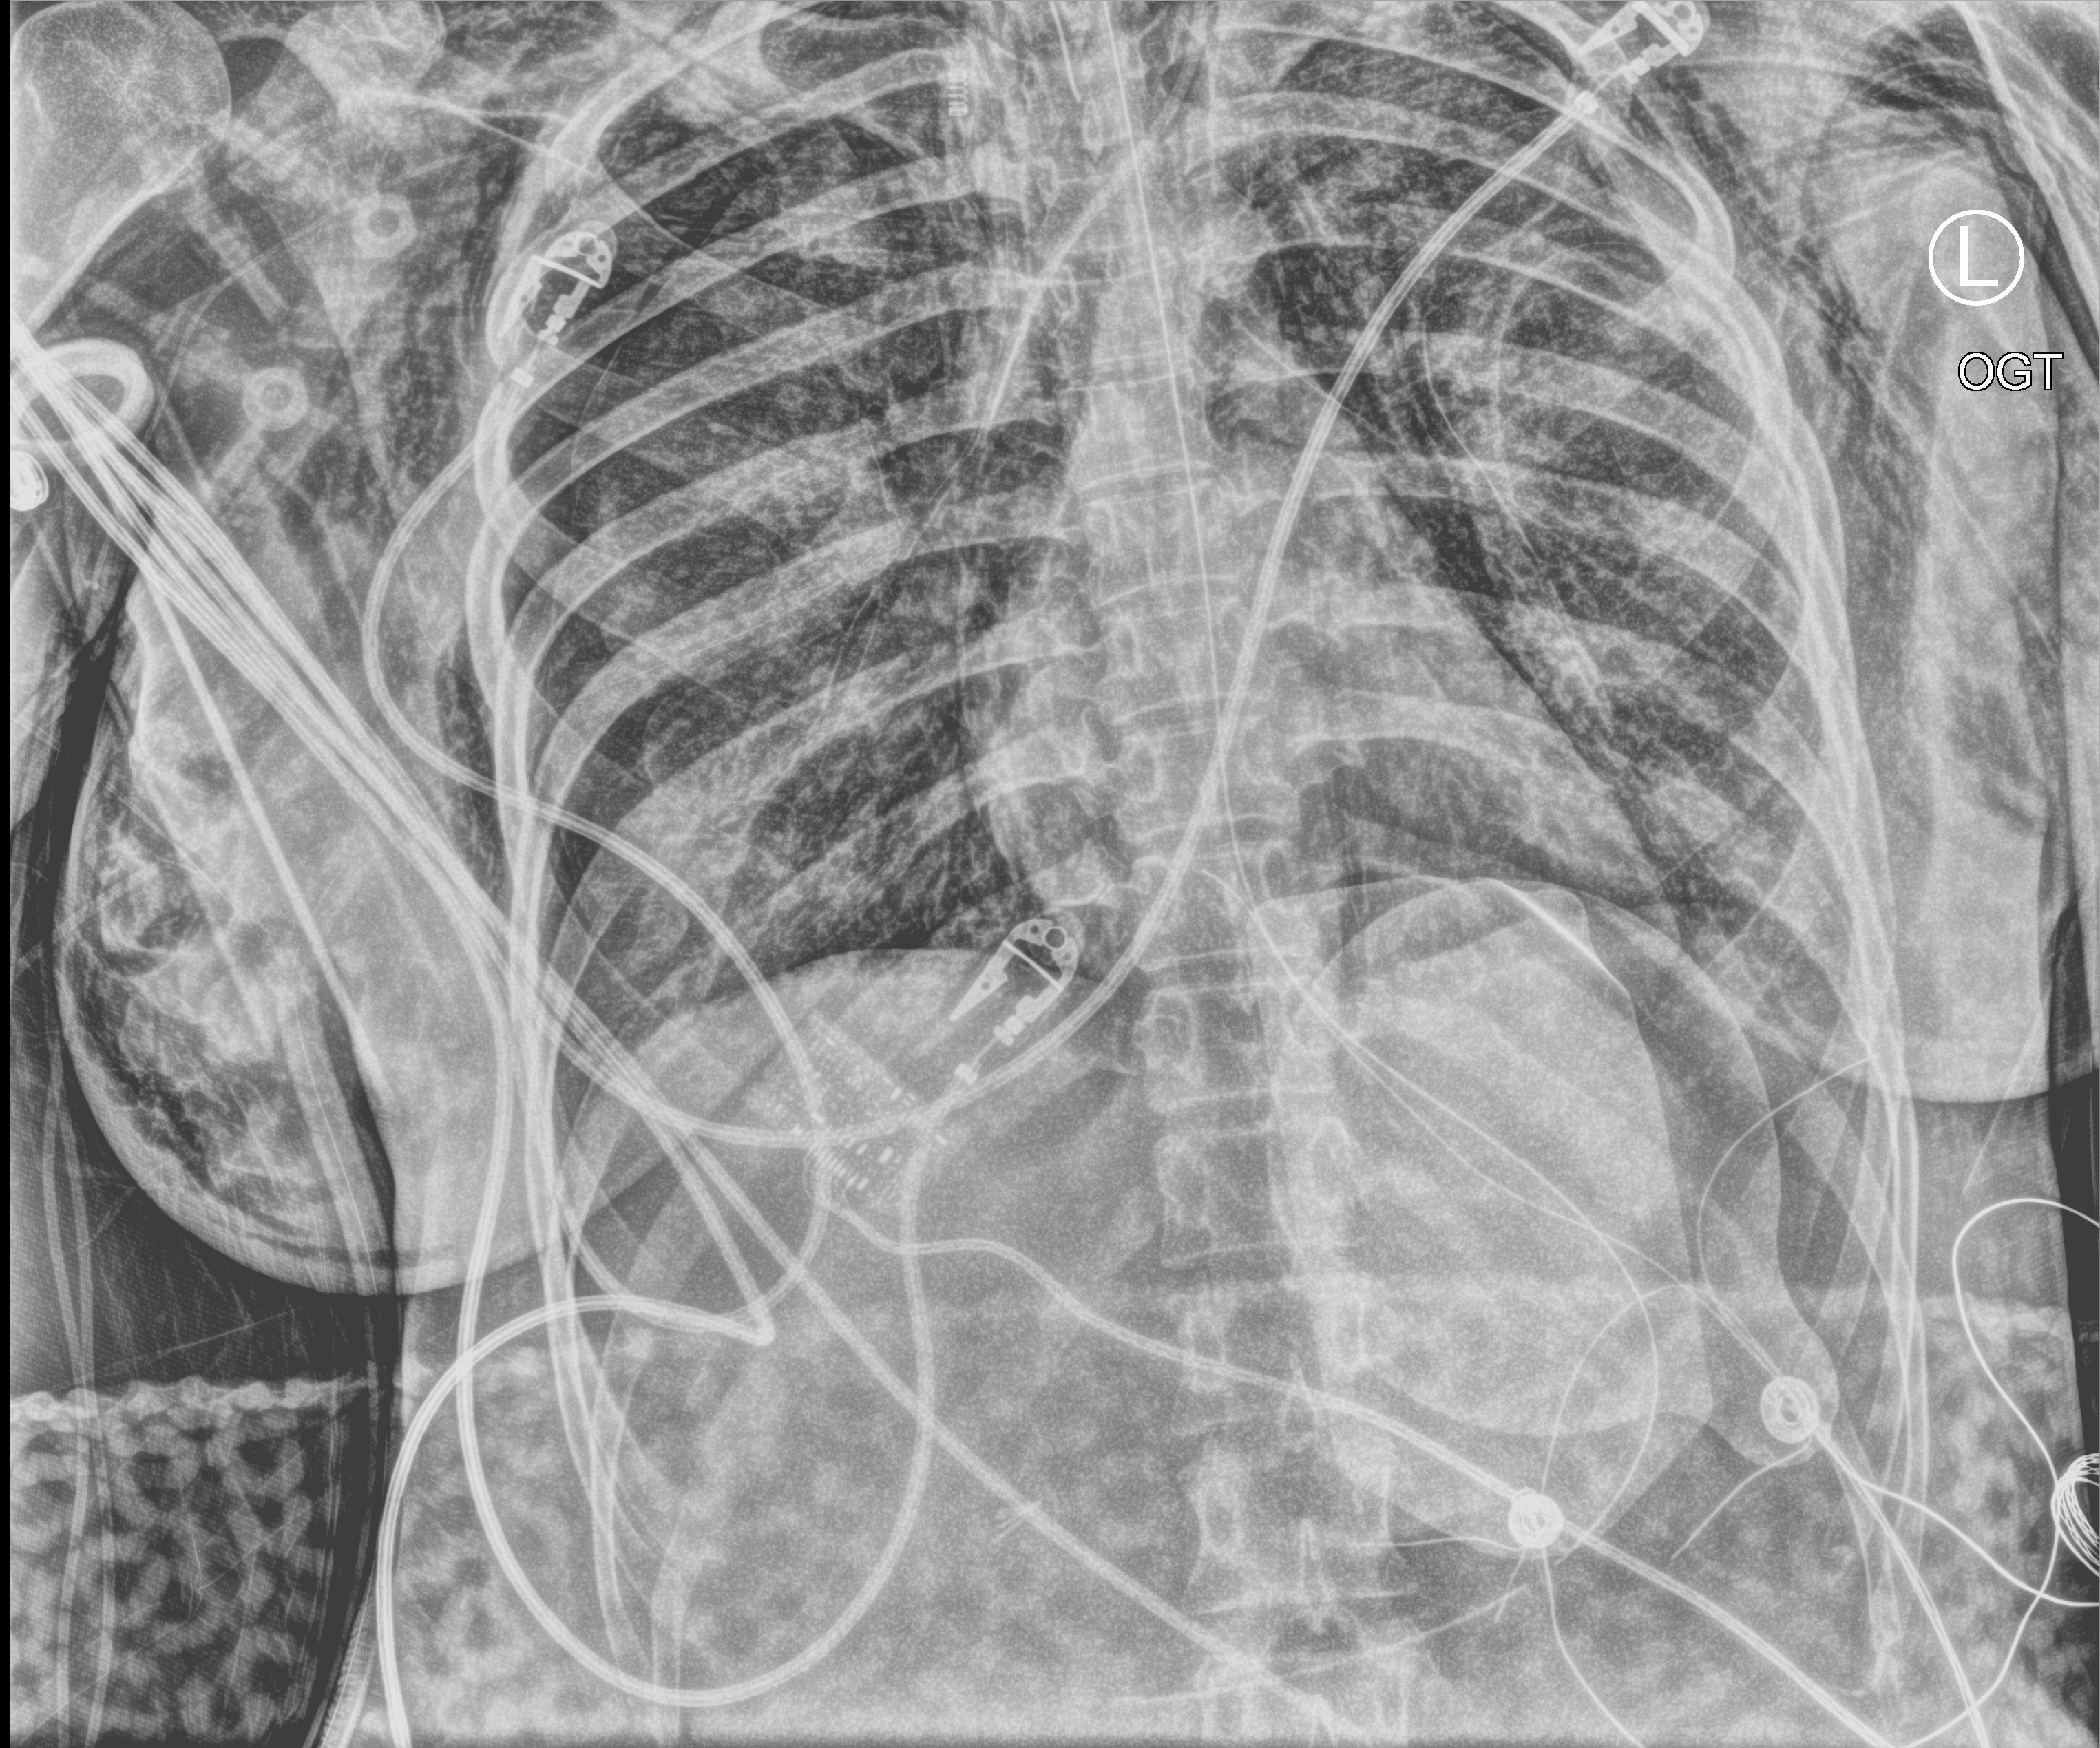
Chest X-ray (portable); anteroposterior (AP) projection. Adult patient hospitalised with COVID-19, age 18–59 years.
Admission-level facts for this patient (not findings on this image; timing relative to this image not recorded):
- smoking status (admission record): never